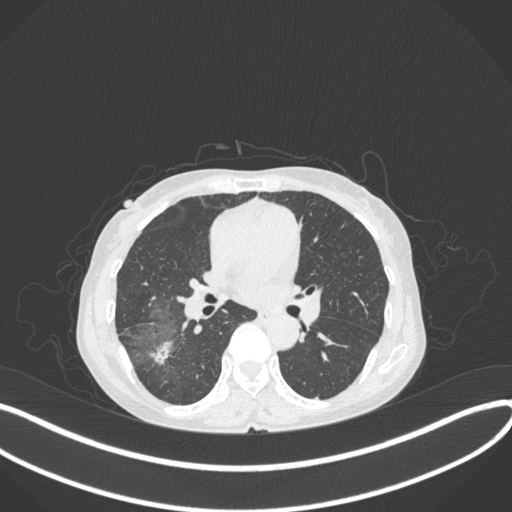
Chest CT, one axial slice. Position 210 of 379 along the scan axis. 120 kVp. Lung window (W 1500 / L -600 HU). 1 mm slice thickness. 512 × 512 image matrix, field of view 400 × 400 mm. Female patient, age 69 years. From the clinical record (not read from this slice): clinical TNM (as recorded): T1b N0 M0; histopathological grade: G2-3.
Outlined on this slice (rectangle marked by the reading radiologist):
- lung tumour (recorded histology: adenocarcinoma): bounding box (x1, y1, x2, y2) in pixels: (148, 337, 176, 368)